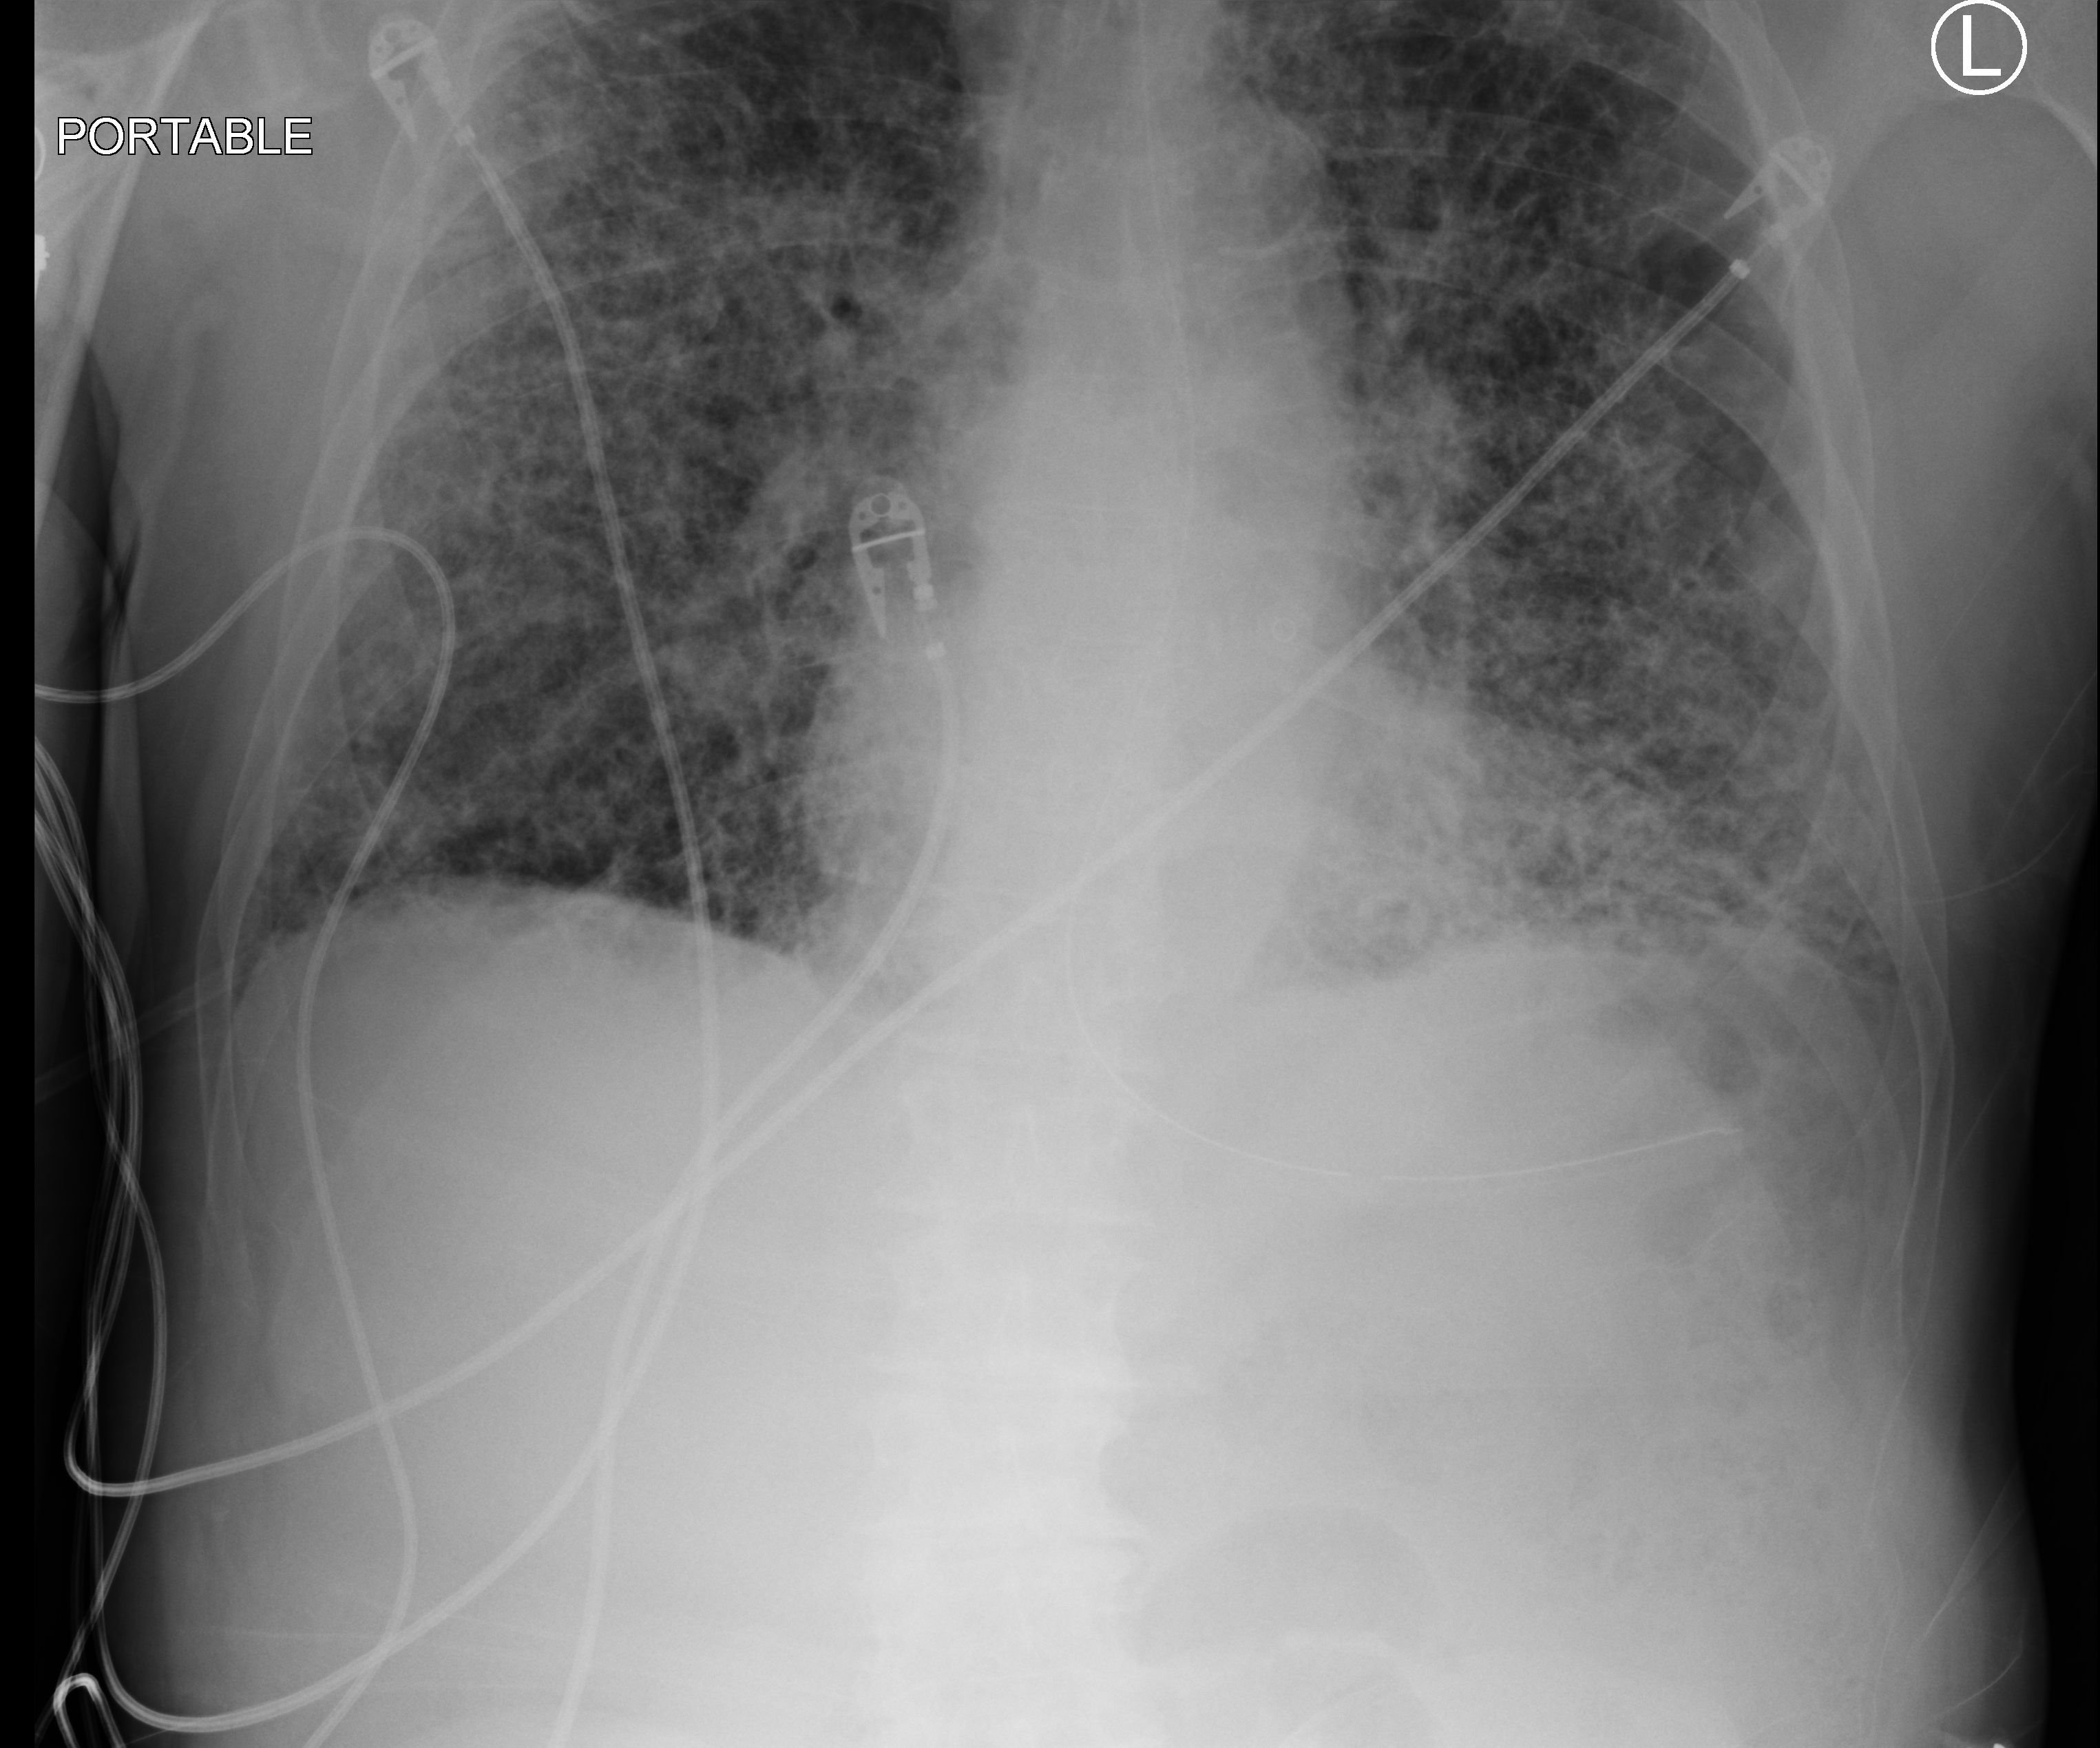
Portable chest radiograph, anteroposterior (AP) projection. Patient hospitalised with COVID-19; male, aged 75–90 years.
From the hospital-stay record, not from the radiograph (when in the stay this image was taken is not recorded): smoking status (admission record): never.